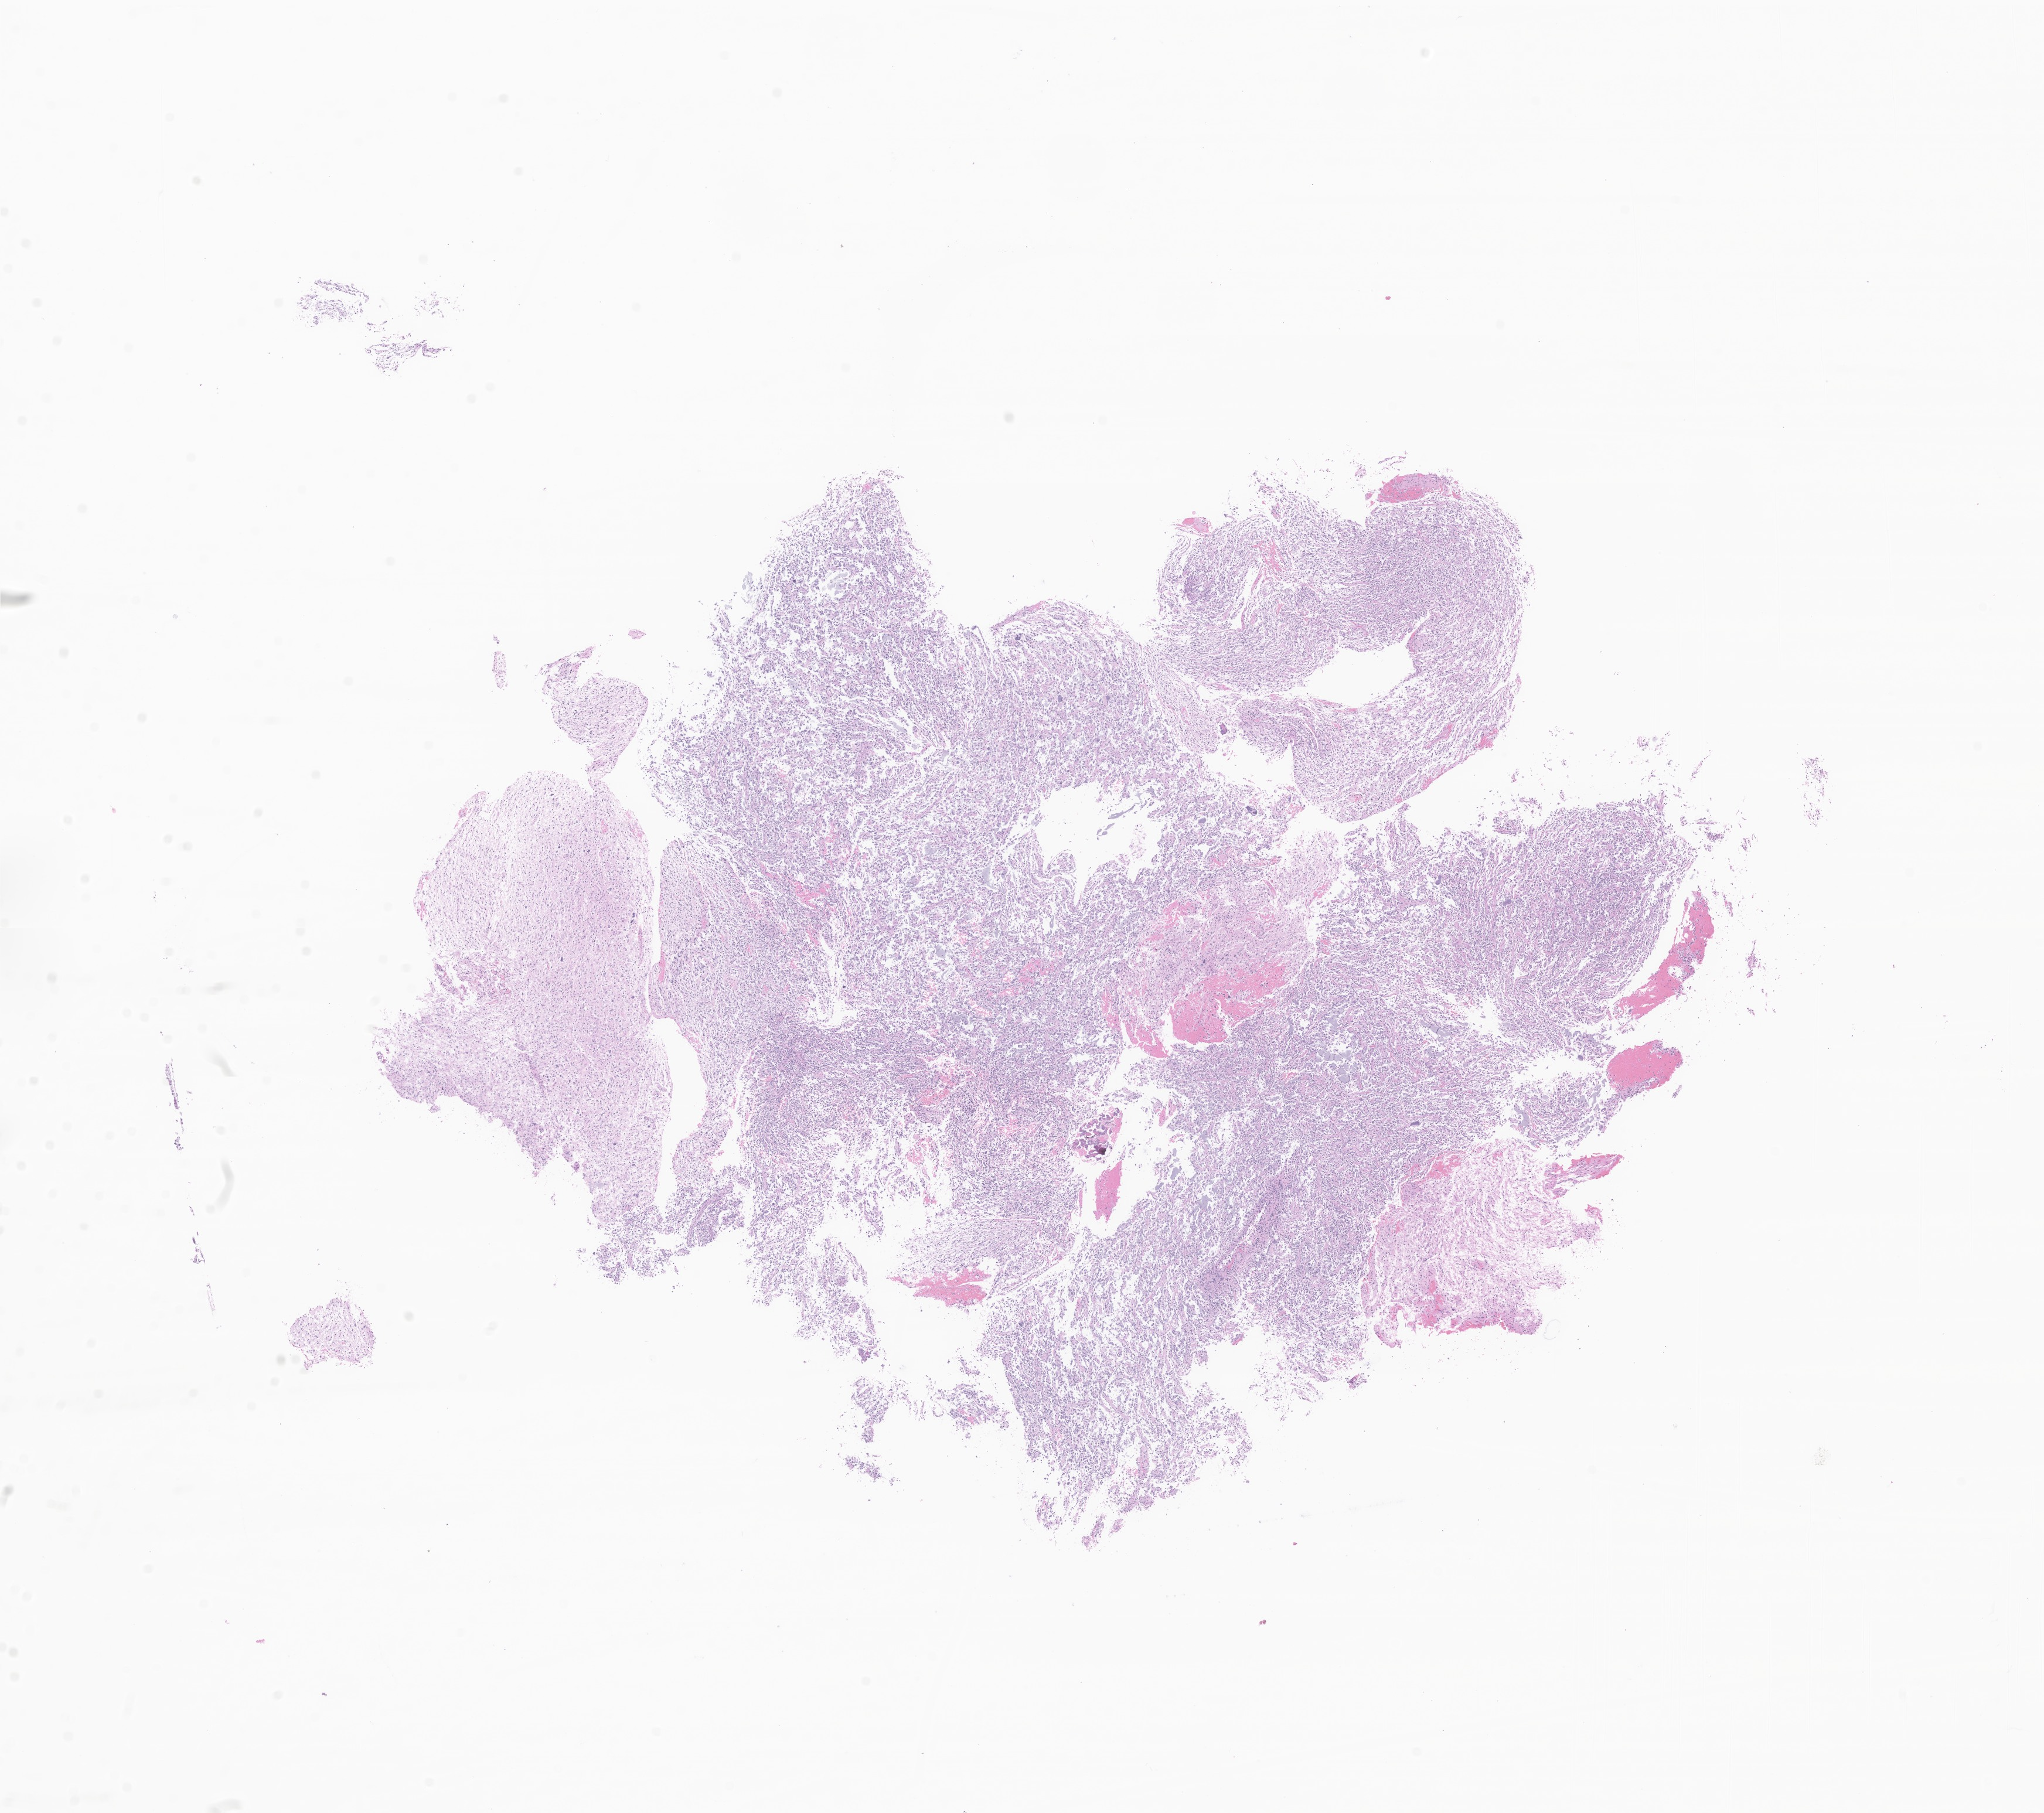
H&E whole-slide image of tumor tissue from the brain — shown as a low-resolution overview of the whole scanned area (about 14.7 x 13.0 mm). Formalin-fixed paraffin-embedded section. Patient female; age 202 months (16 years 10 months).
Diagnosis: Glioma, malignant.